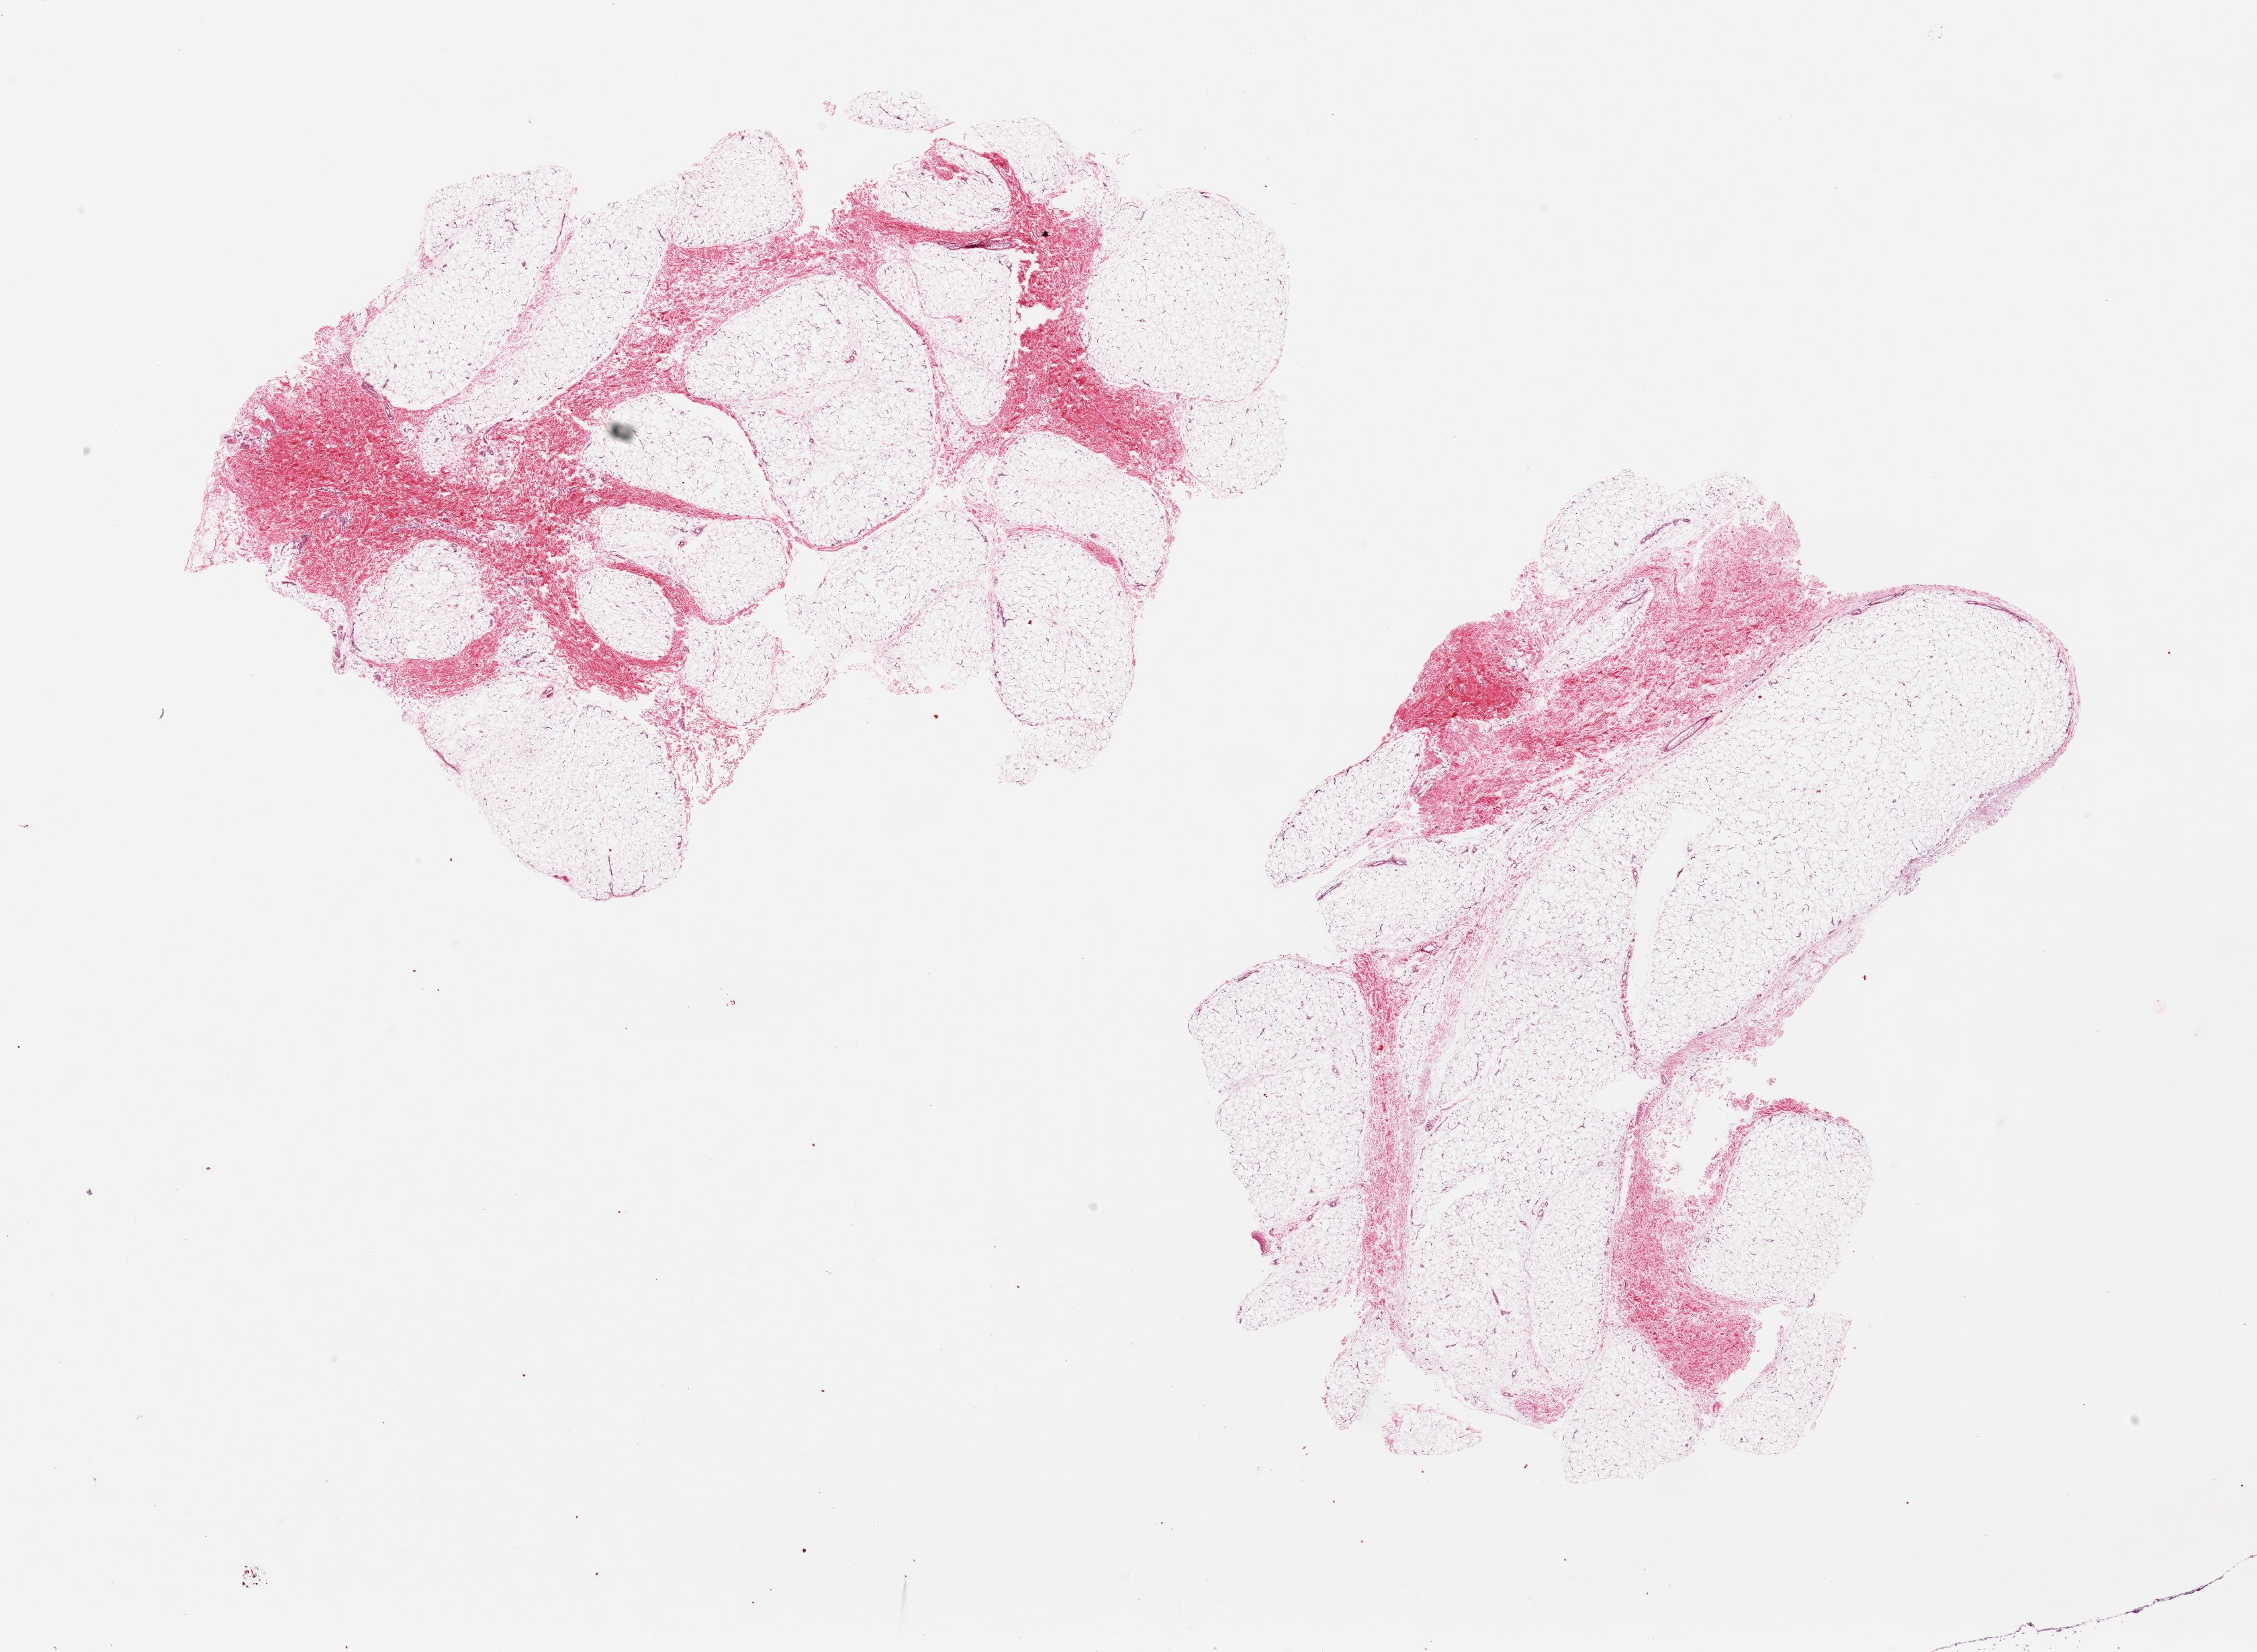
Digitized H&E-stained section, whole scanned area (about 26.6 x 19.5 mm) shown as a low-resolution overview; PAXgene-fixed, paraffin-embedded tissue; sampled site (target tissue): adipose tissue; tissue donor sample. Donor: male.
Review note (as recorded): 2 aliquots, ~10x9mm.